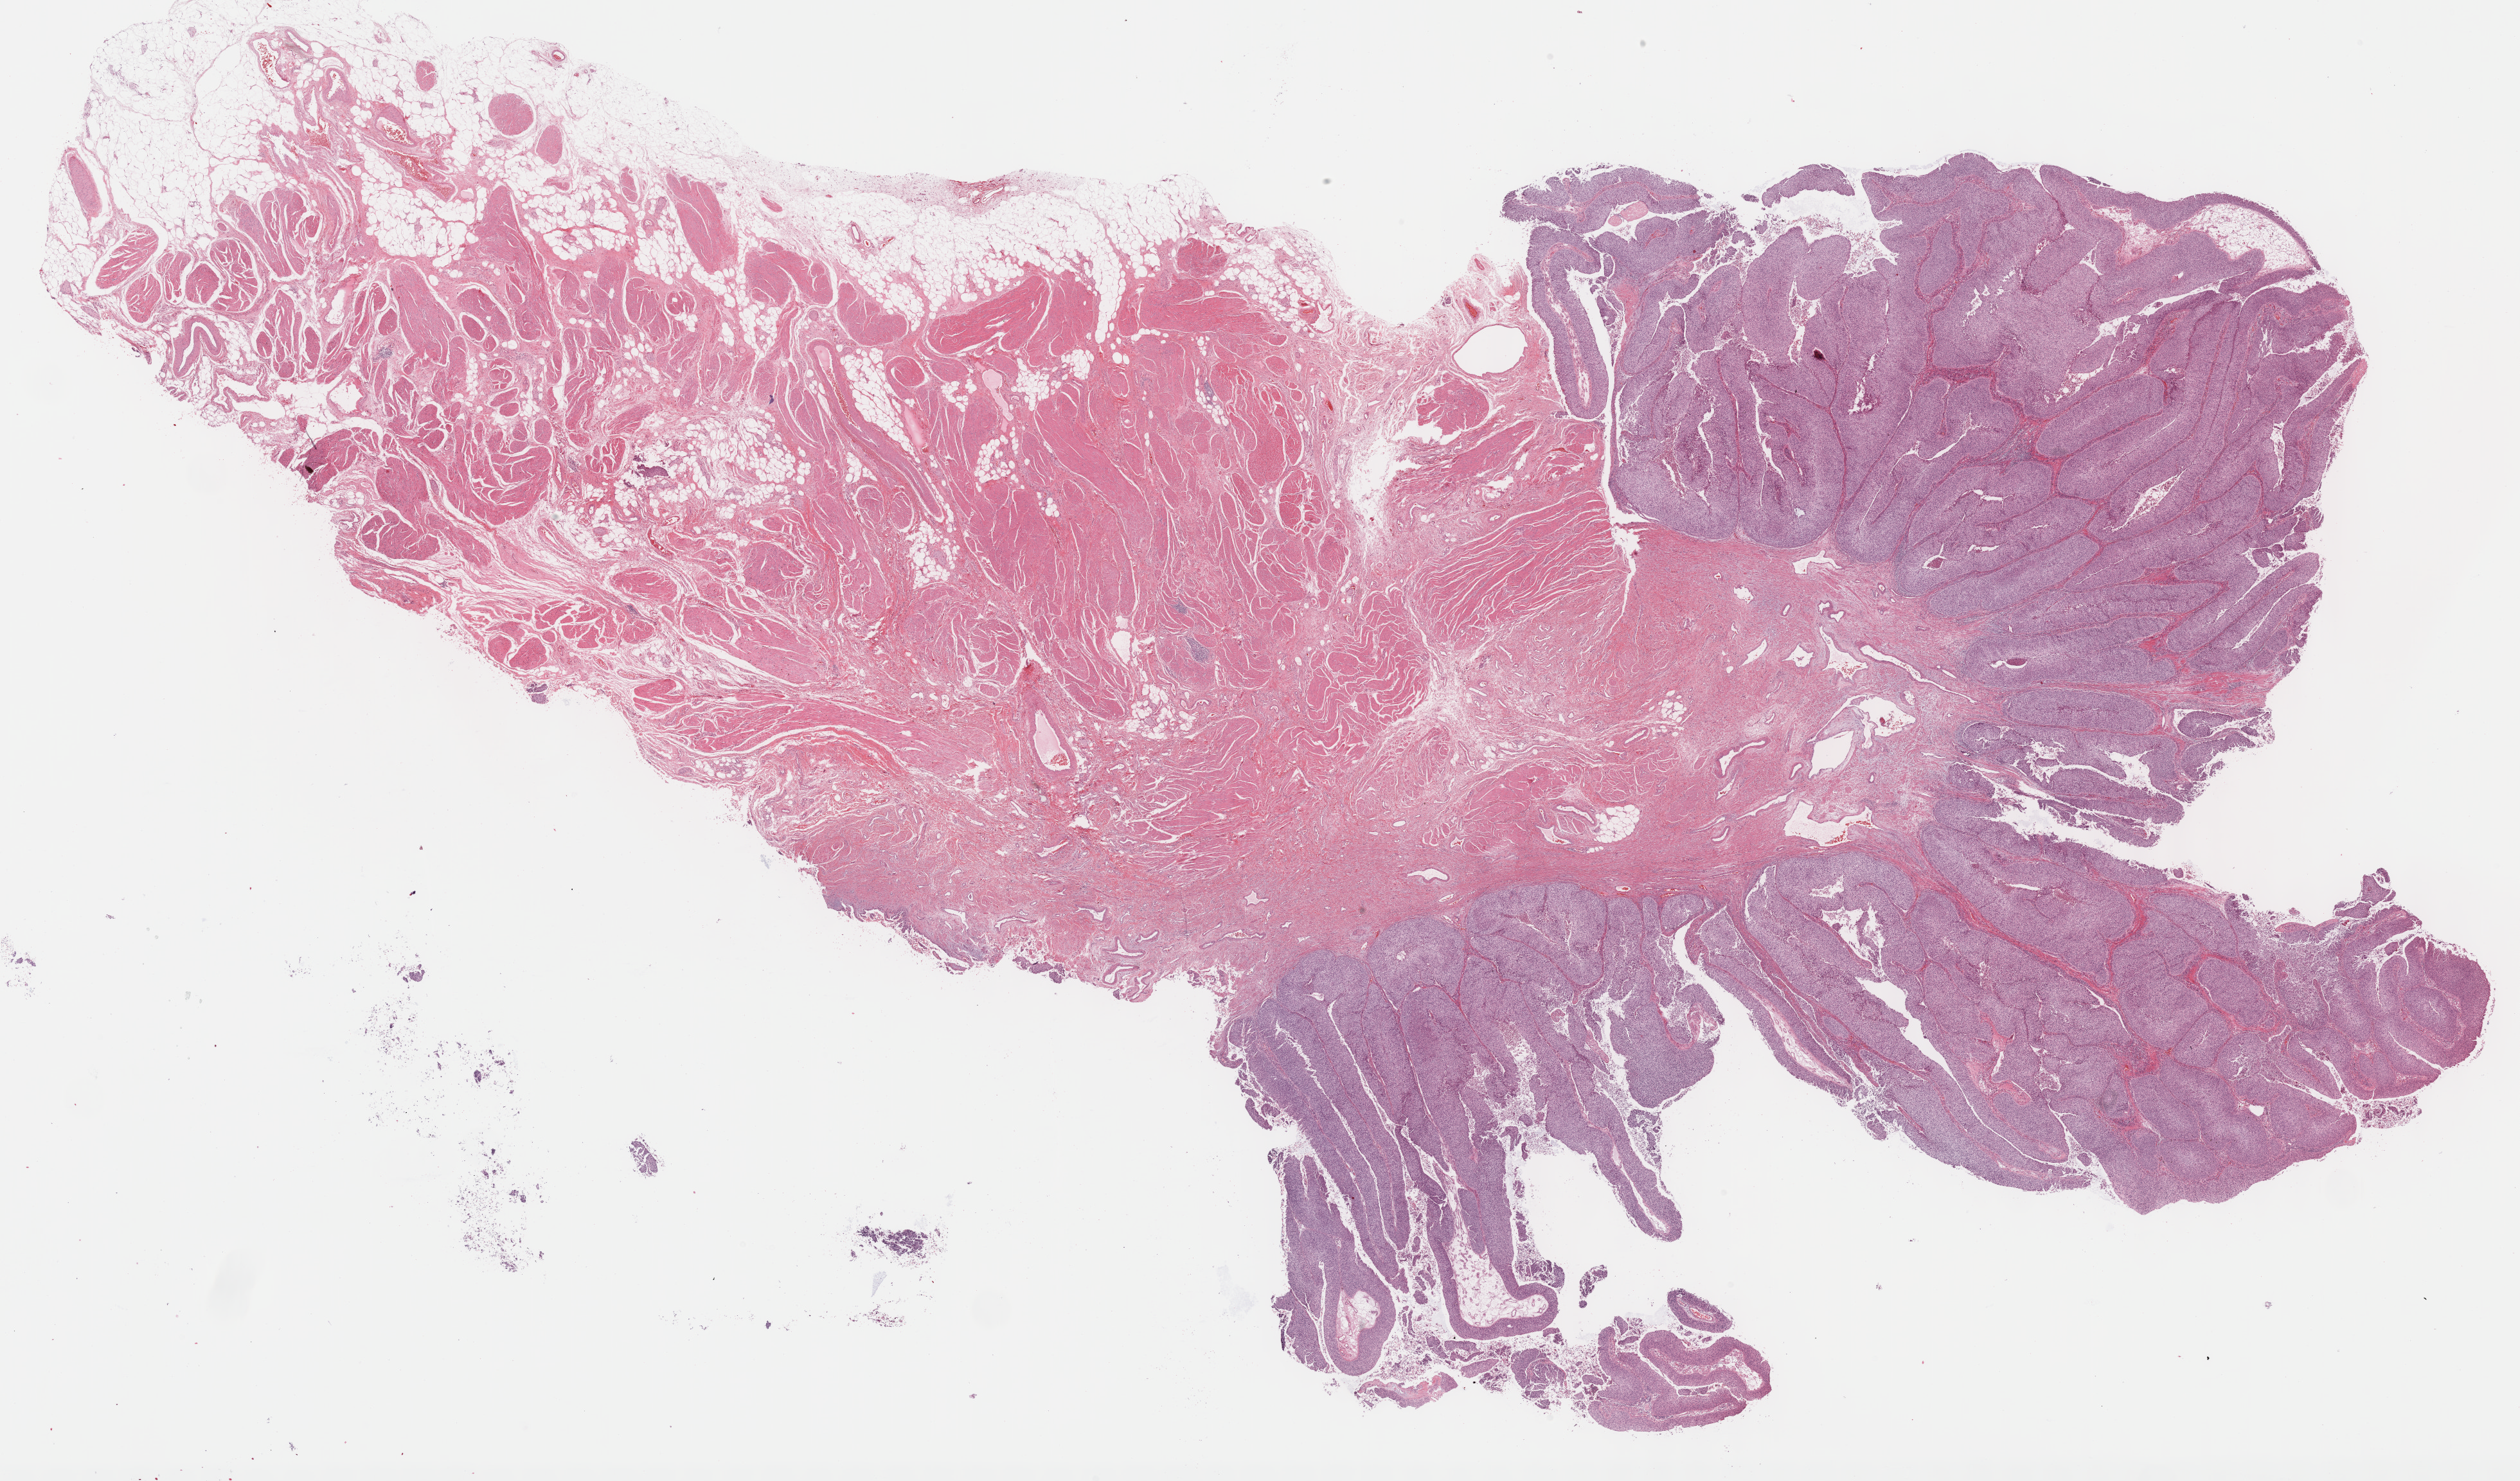
Digitized H&E-stained tissue section (whole slide) — shown as a low-resolution overview of the whole scanned area (about 31.7 x 18.6 mm), formalin-fixed paraffin-embedded (FFPE) diagnostic section, bladder, primary tumour sample. Female patient; age at initial diagnosis 75 years.
Diagnosis: Papillary transitional cell carcinoma.